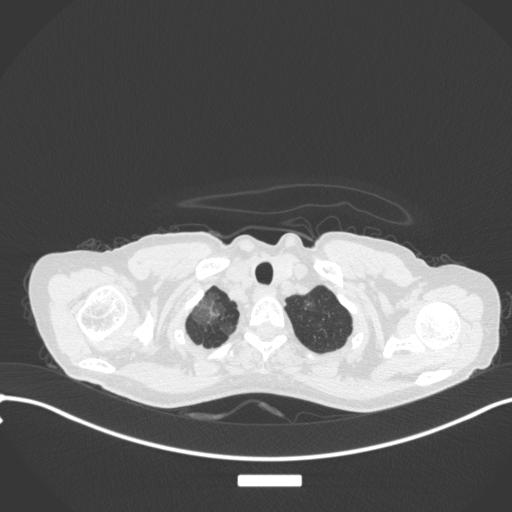
Chest CT, one axial slice; position 309 of 311 along the scan axis; lung window (W 1500 / L -600 HU); 1 mm slice thickness; 512 × 512 image matrix. Female patient, age 59 years. Case-level facts recorded for this patient, not image findings: clinical TNM (as recorded): T3 N0 M0; histopathological grade: G1.
Outlined on this slice (rectangle marked by the reading radiologist):
- lung tumour (recorded histology: adenocarcinoma): bounding box (x1, y1, x2, y2) in pixels: (188, 294, 225, 330)